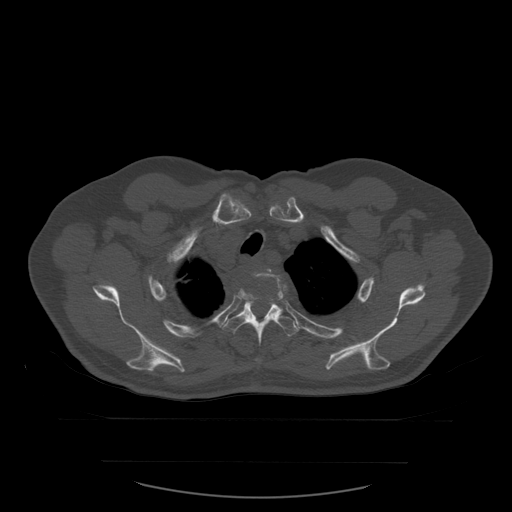
CT including the spine, one axial slice; bone window (W 1800 / L 400 HU); 1.25 mm slice thickness; 512 × 512 image matrix, field of view 479 × 479 mm. Patient age 71 years. From the clinical record (not read from this slice): primary cancer: lung.
Outlined on this slice (semi-automatically segmented with operator editing):
- T2 vertebra: box from (x=267, y=269) to (x=280, y=280) px
- T3 vertebra: (x=238, y=273)–(x=283, y=313)
- T4 vertebra: (x=222, y=293)–(x=299, y=362)